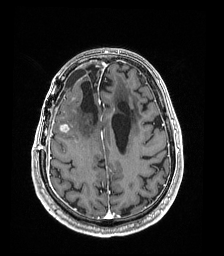
Brain MRI from a brain-tumour surgery series, one axial slice. T1-weighted post-contrast. 1 mm slice thickness. 224 × 256 image matrix, field of view 224 × 256 mm. Case-level facts recorded for this patient, not image findings: histopathology: Astrocytoma; WHO grade: 4; IDH mutation: yes; tumour location: Right Frontal.
Annotated regions visible in this slice (manually delineated by an expert):
- previous resection cavity: bounding box (x1, y1, x2, y2) in pixels: (81, 68, 98, 122)